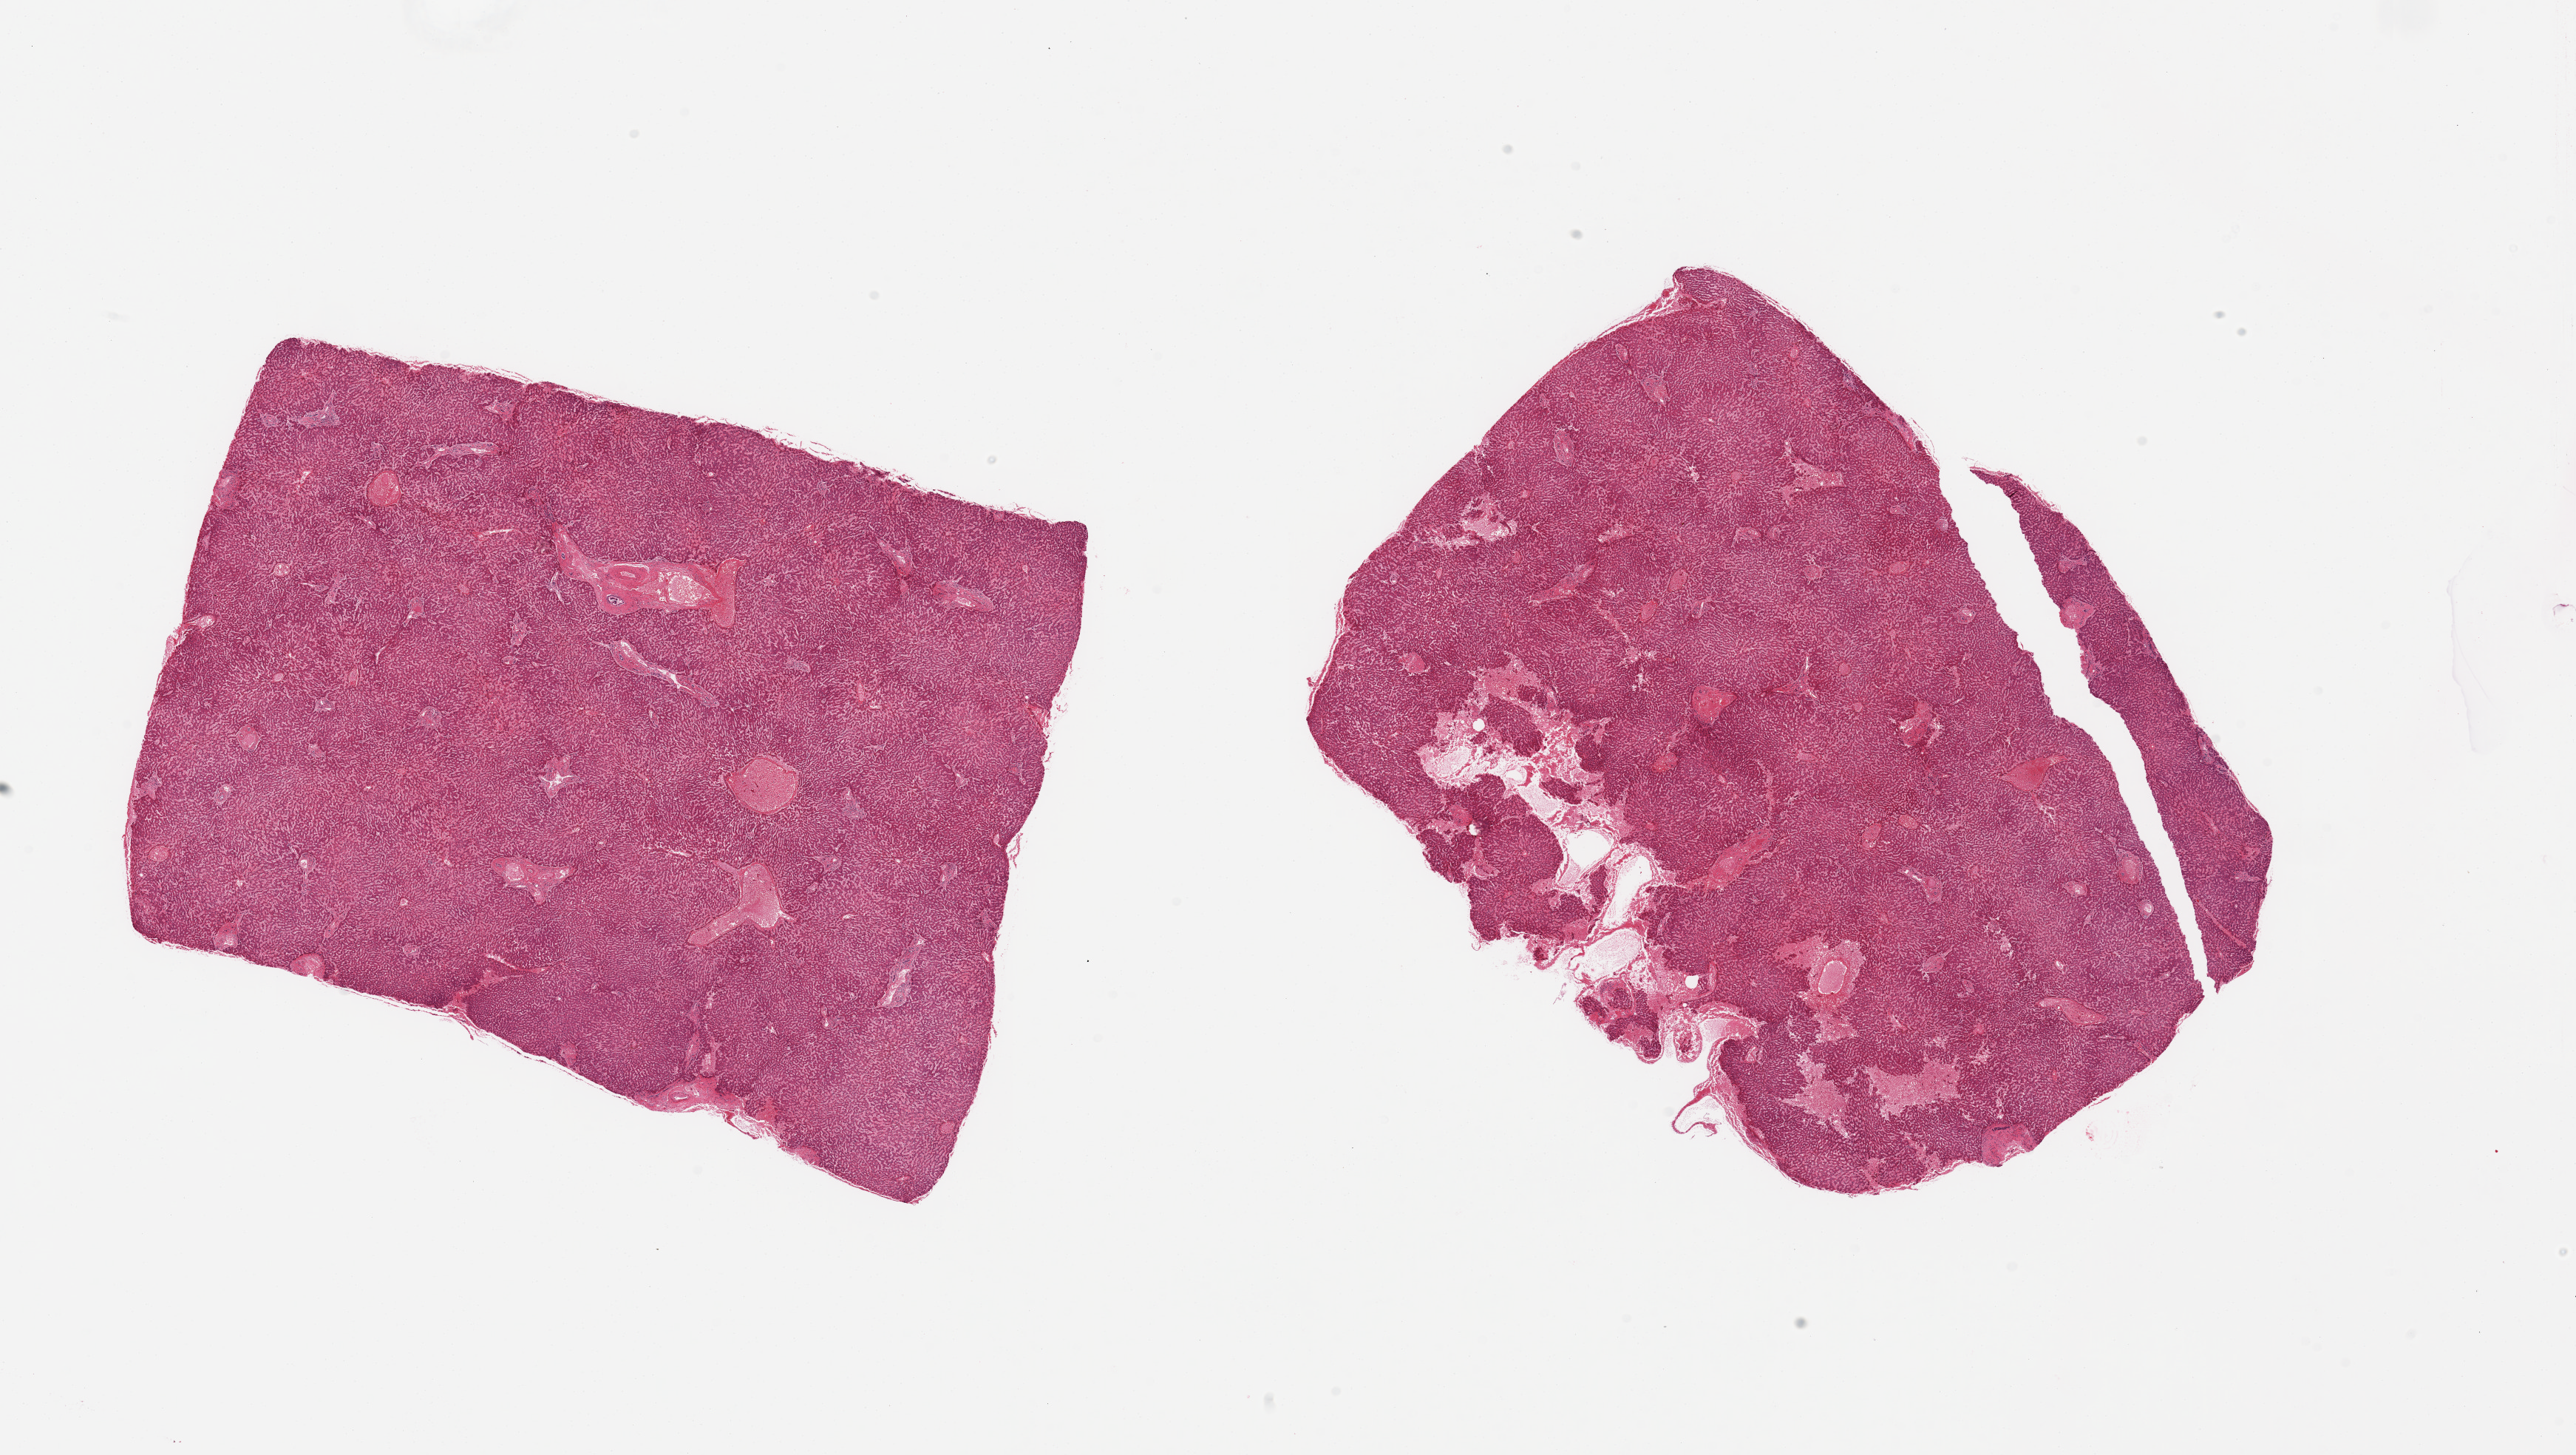
Hematoxylin and eosin (H&E) whole-slide image, brightfield, whole scanned area (about 27.6 x 15.6 mm) shown as a low-resolution overview, PAXgene-fixed paraffin-embedded (PFPE) section, section of liver (target tissue), tissue donor sample. Donor: male.
Pathologist's review note for this sample: 2 pieces; central congestion and hemorrhage.